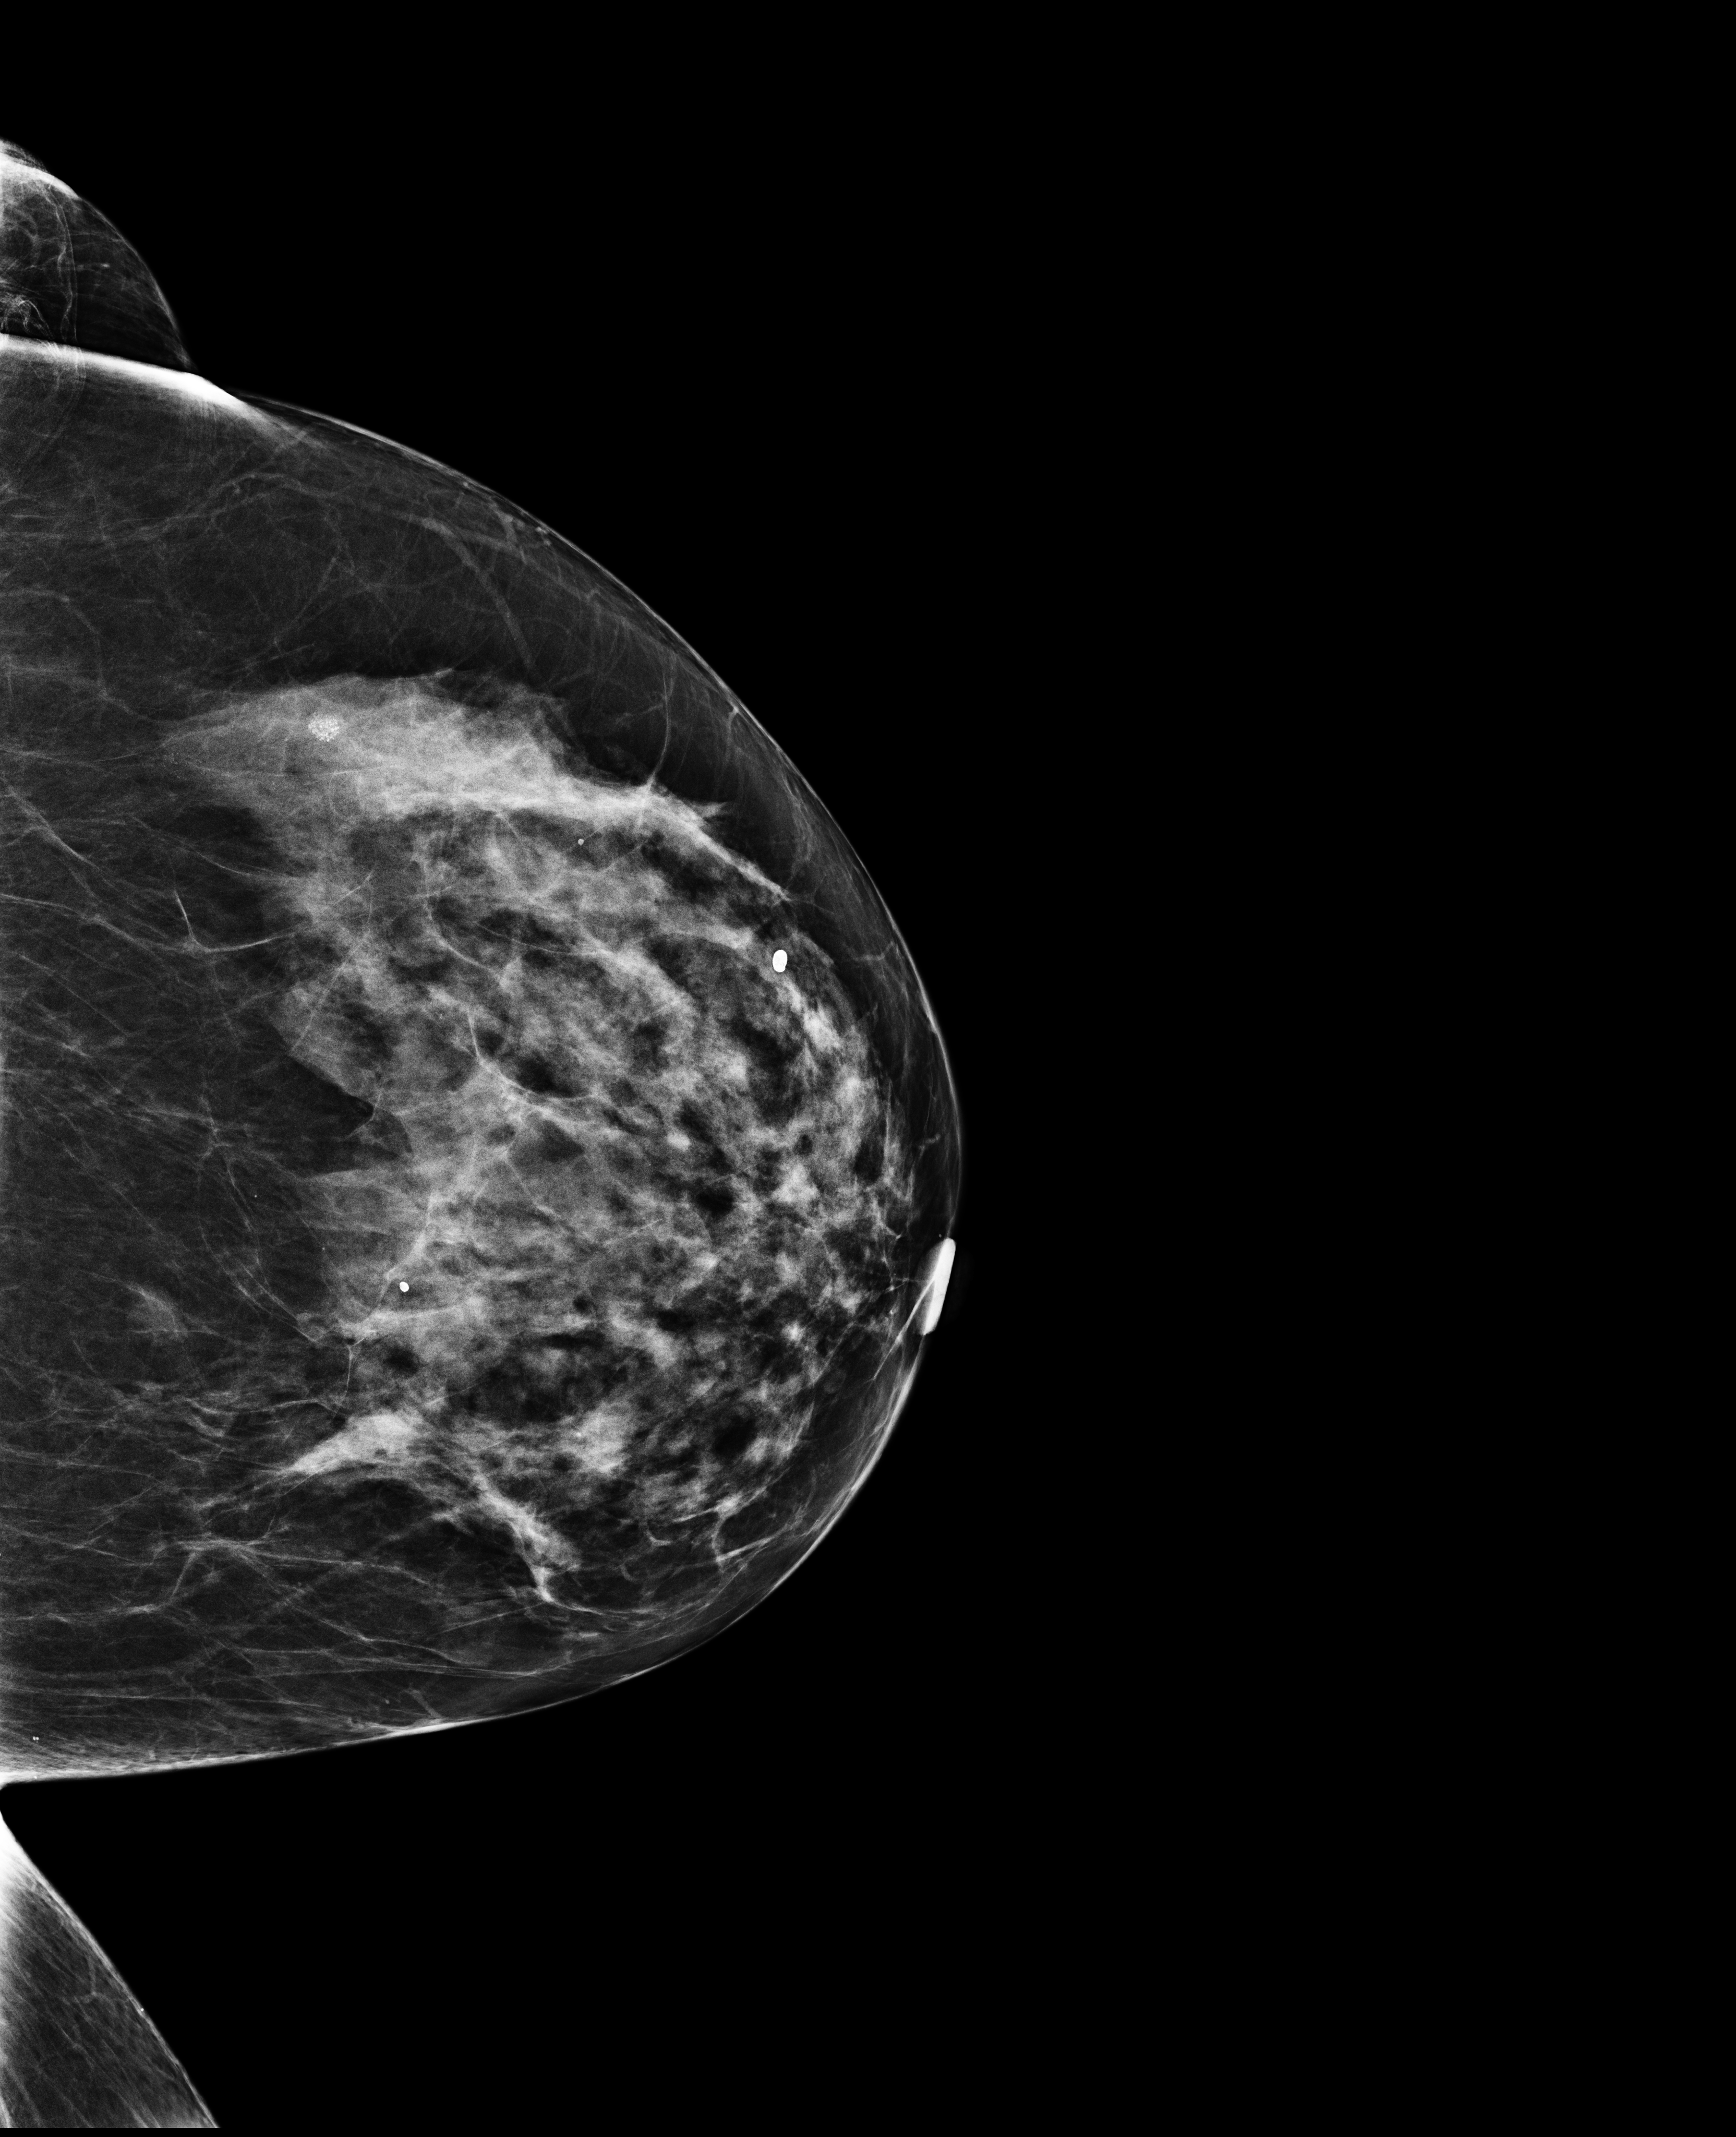
Annual screening mammography examination. Female patient, age 62 years.
Image type: full-field digital mammogram. Breast: left. Projection: cranio-caudal projection.